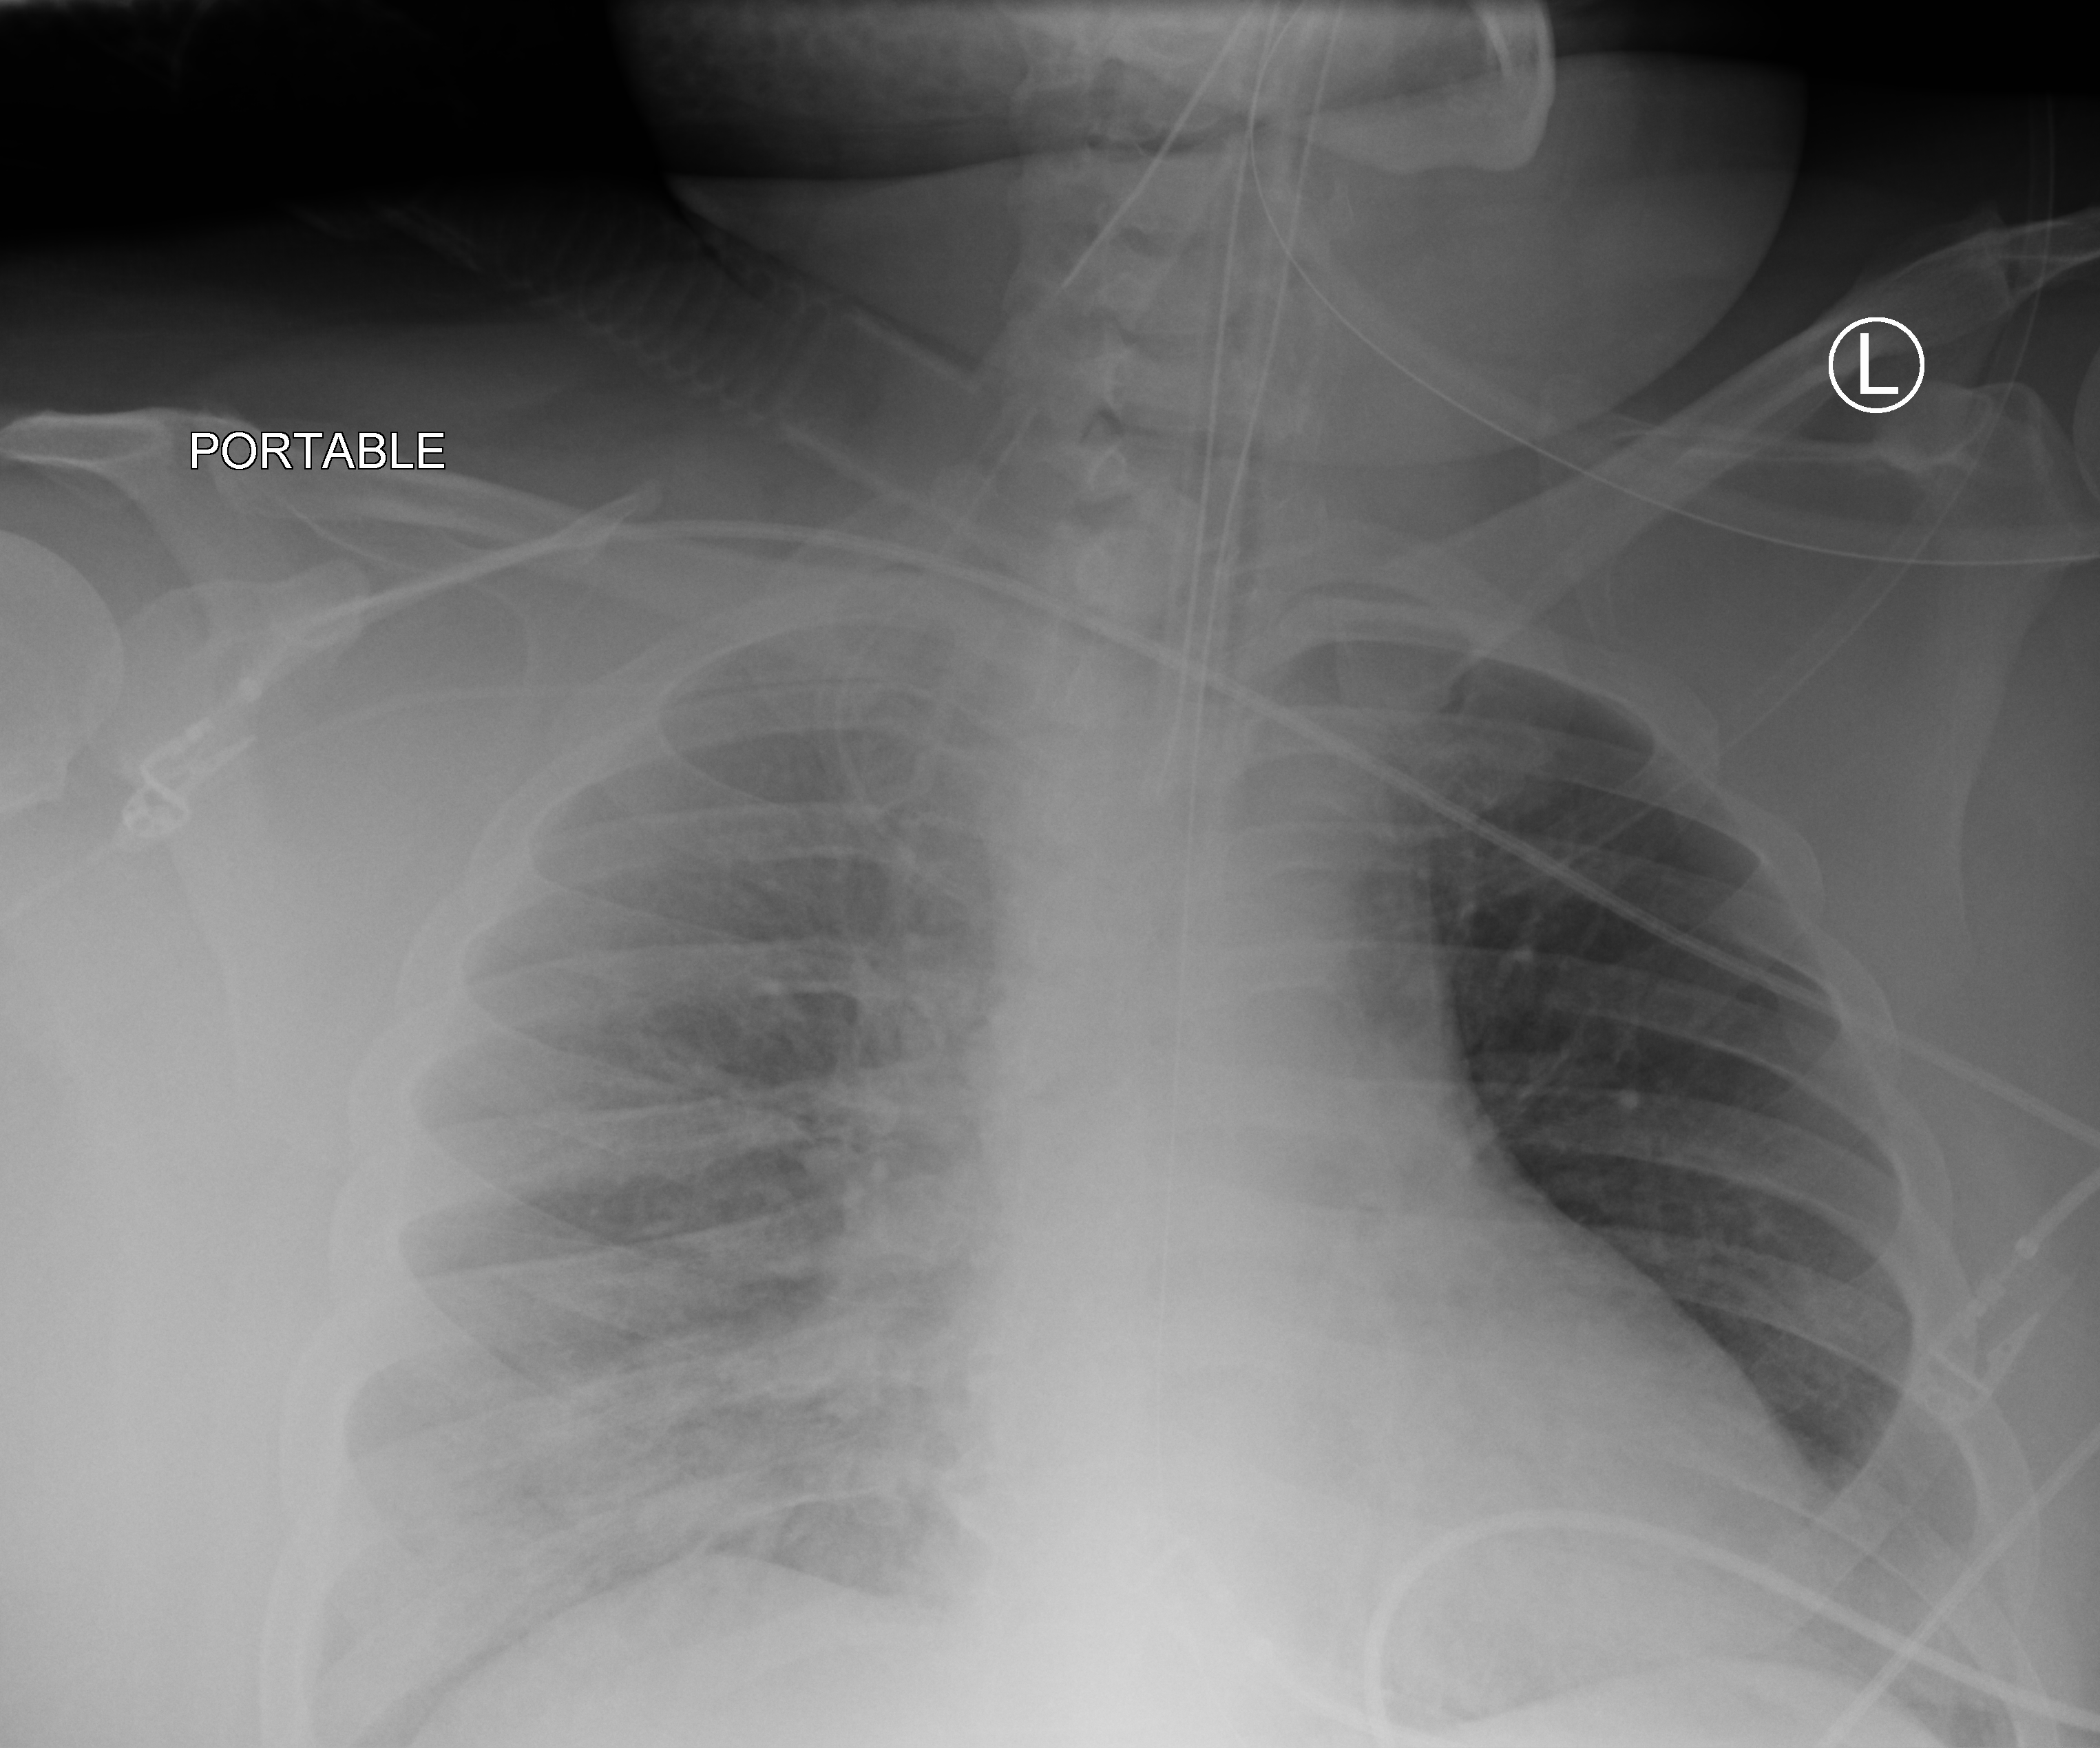
Chest X-ray (portable); anteroposterior (AP) projection. Adult patient hospitalised with COVID-19, age 18–59 years.
From the hospital-stay record, not from the radiograph (when in the stay this image was taken is not recorded): mechanically ventilated during this hospital stay: yes; length of hospital stay: 10 days; admitted to intensive care during this hospital stay: yes.